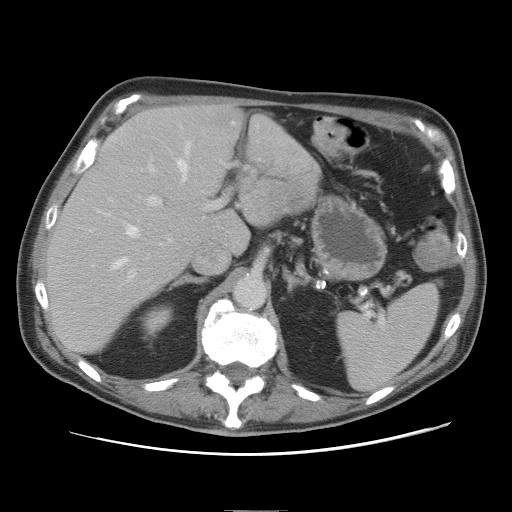
Contrast-enhanced abdominal CT, one axial slice. 120 kVp. Intravenous contrast given. Soft-tissue window (W 400 / L 40 HU). 5 mm slice thickness. 512 × 512 image matrix. Male patient, age 69 years. Case-level facts recorded for this patient, not image findings: diagnosis: colorectal cancer liver metastases, imaged before liver resection; multiple liver metastases: no; largest metastasis: 8.5 cm.
Outlined on this slice (manually delineated by an expert):
- hepatic veins: bounding box <114,141,191,268> (left, top, right, bottom; pixels)
- liver: <48,106,322,352>
- planned liver remnant (the part of the liver to remain after resection): <48,106,246,351>
- portal vein (with intrahepatic branches): <127,141,260,282>
- liver metastasis: <287,195,298,208>